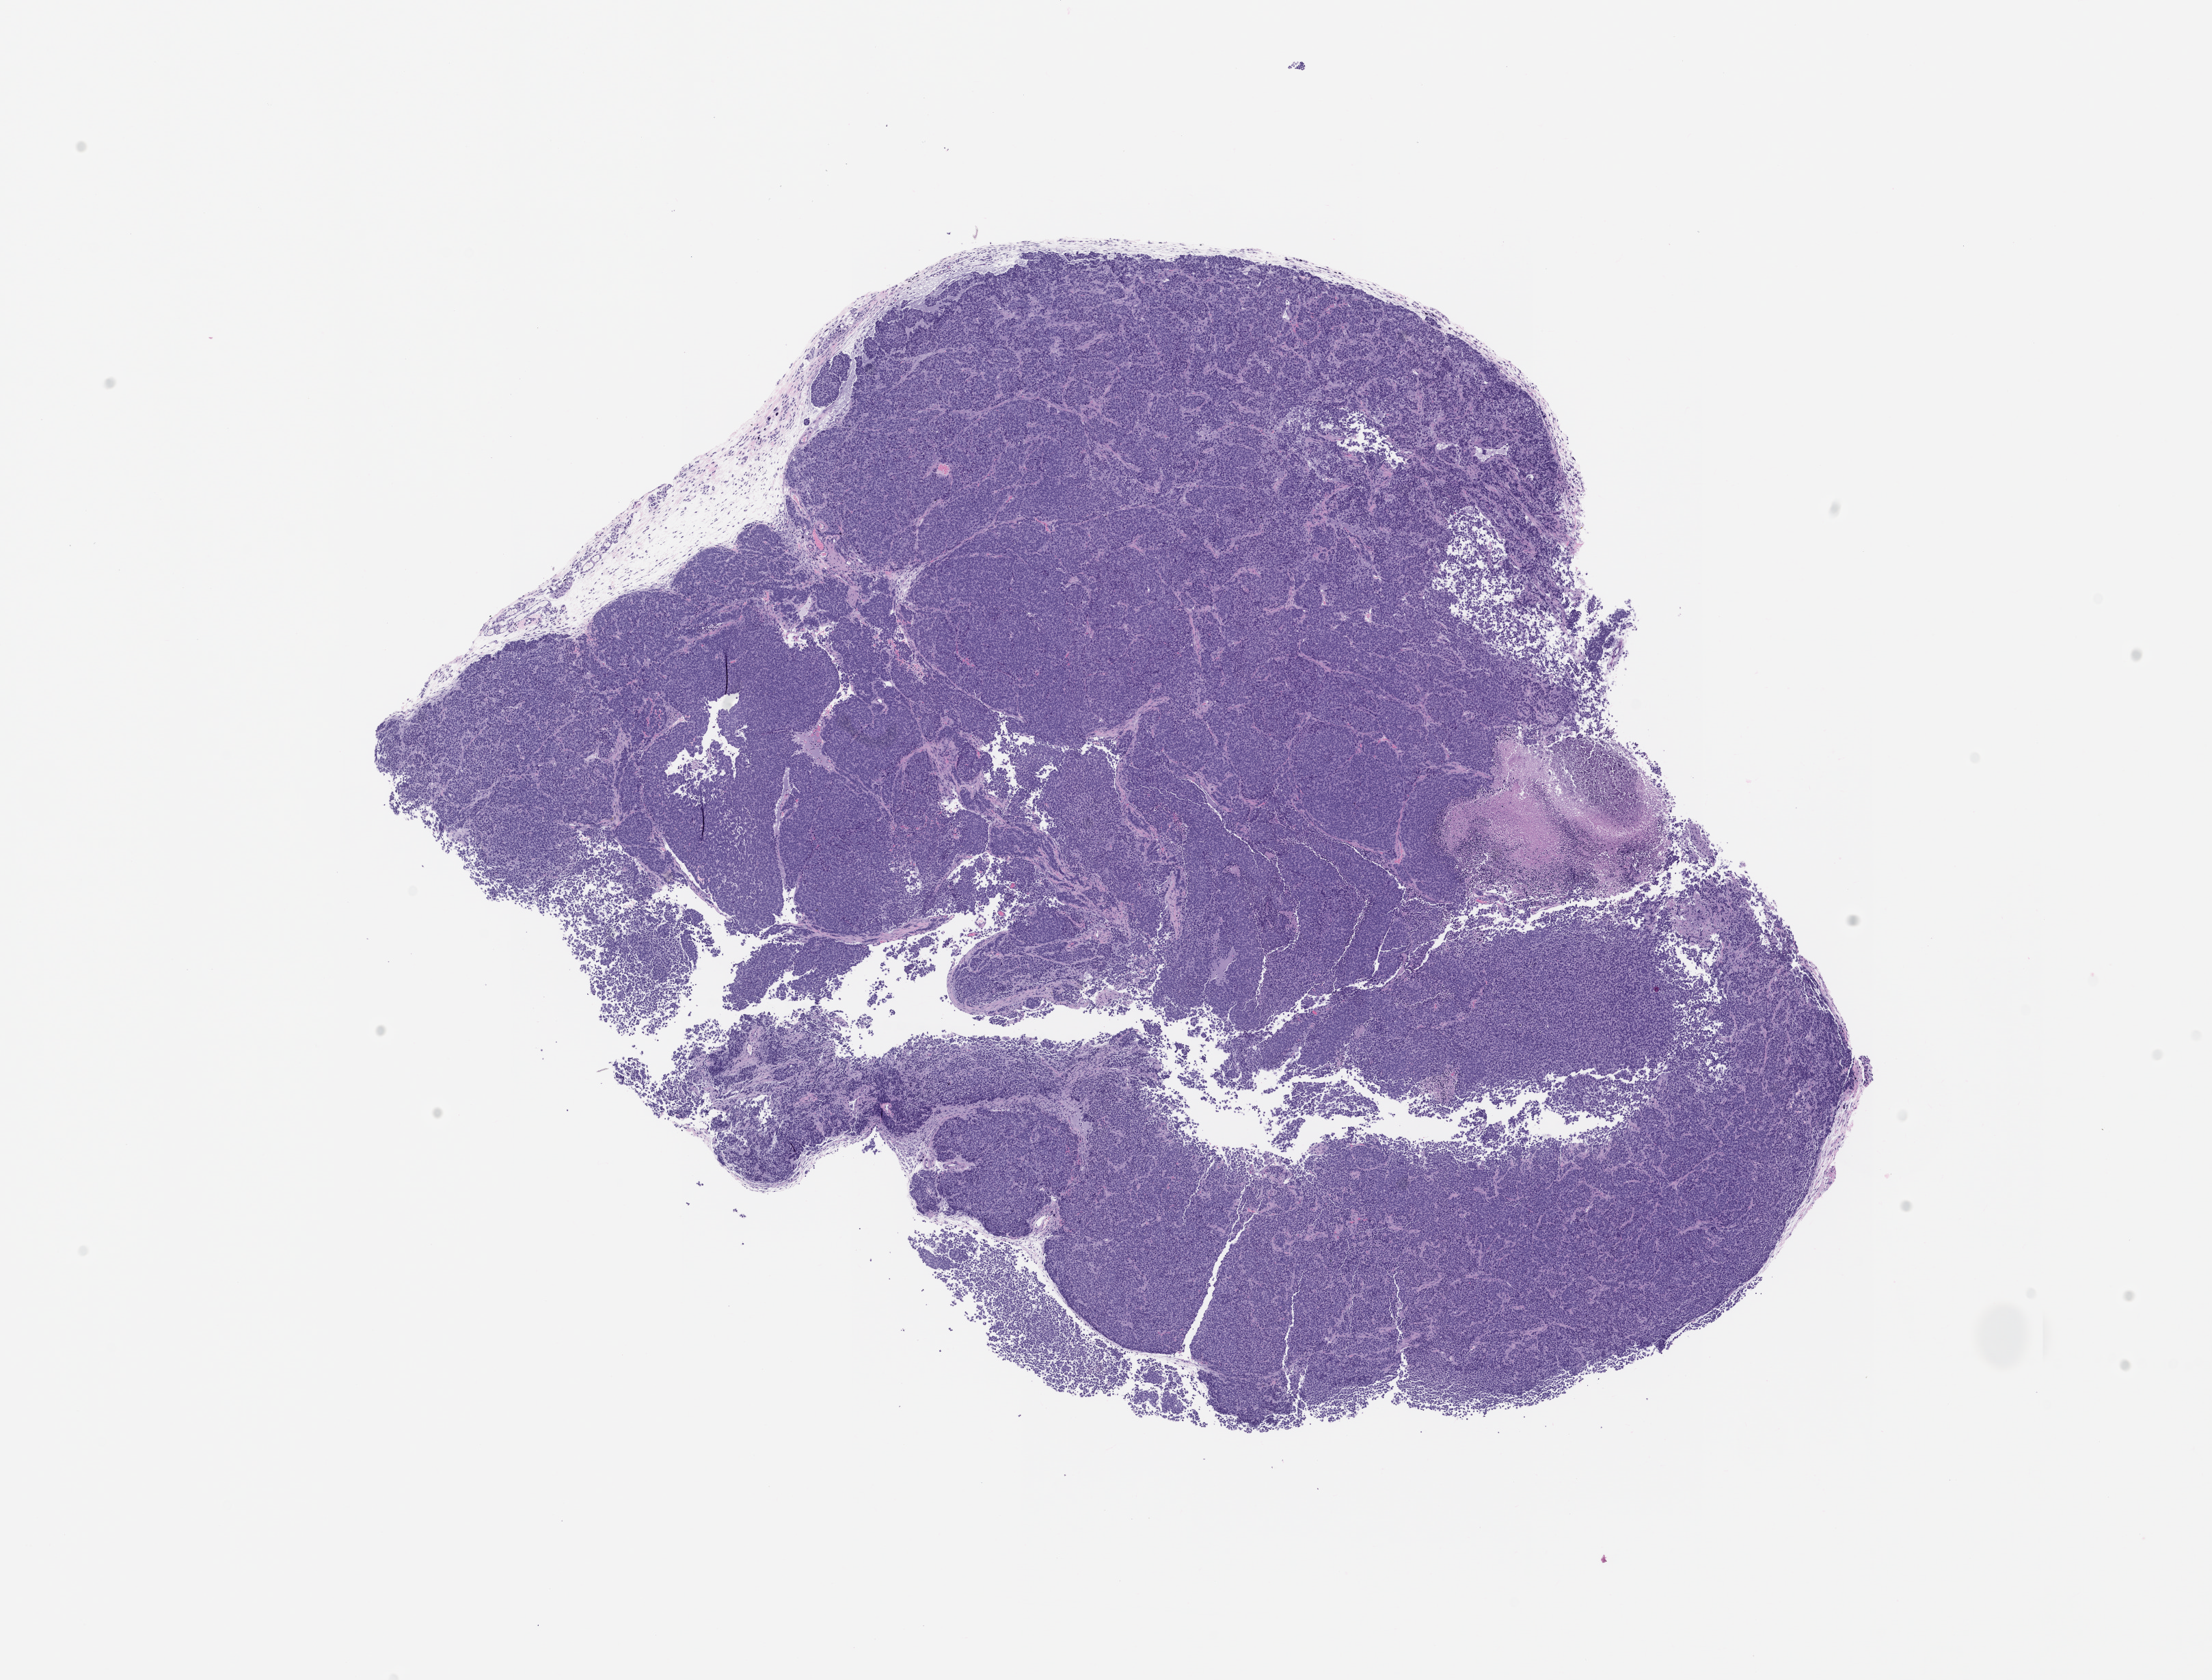
H&E whole-slide image of a patient-derived xenograft (PDX) tumor grown in a mouse, passage 0, a low-resolution overview of the entire scanned area, about 13.0 x 9.8 mm; FFPE section; tumor site category: bladder.
Originating patient diagnosis: Bladder Small Cell Neuroendocrine Carcinoma.